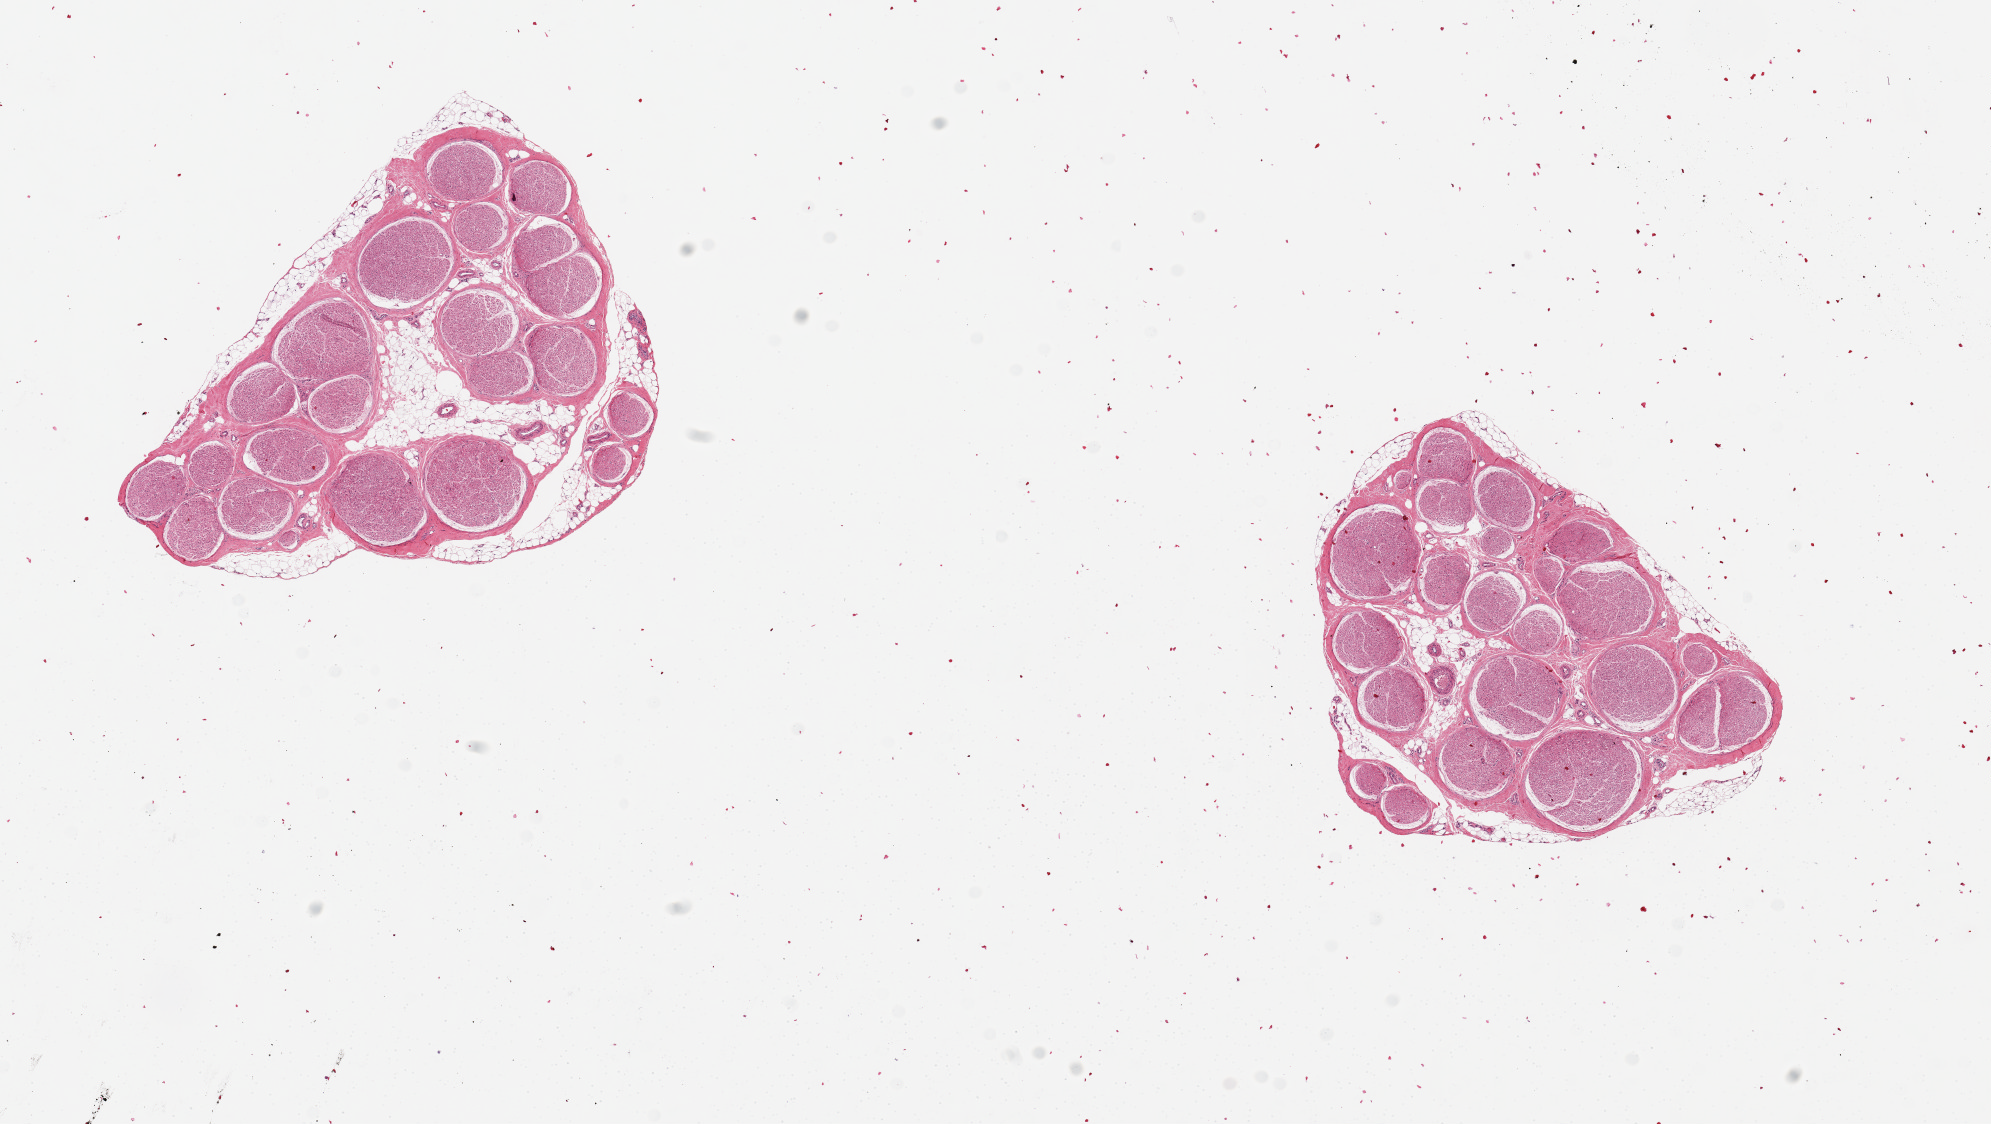
Whole-slide image, hematoxylin and eosin (H&E) stain, low-resolution overview of the scanned area, about 15.8 x 8.9 mm, PAXgene-fixed, paraffin-embedded tissue, sampled site (target tissue): tibial nerve, tissue donor sample. Donor: female.
- review note (as recorded): 2 pieces ~4mm d, relatively clean specimens